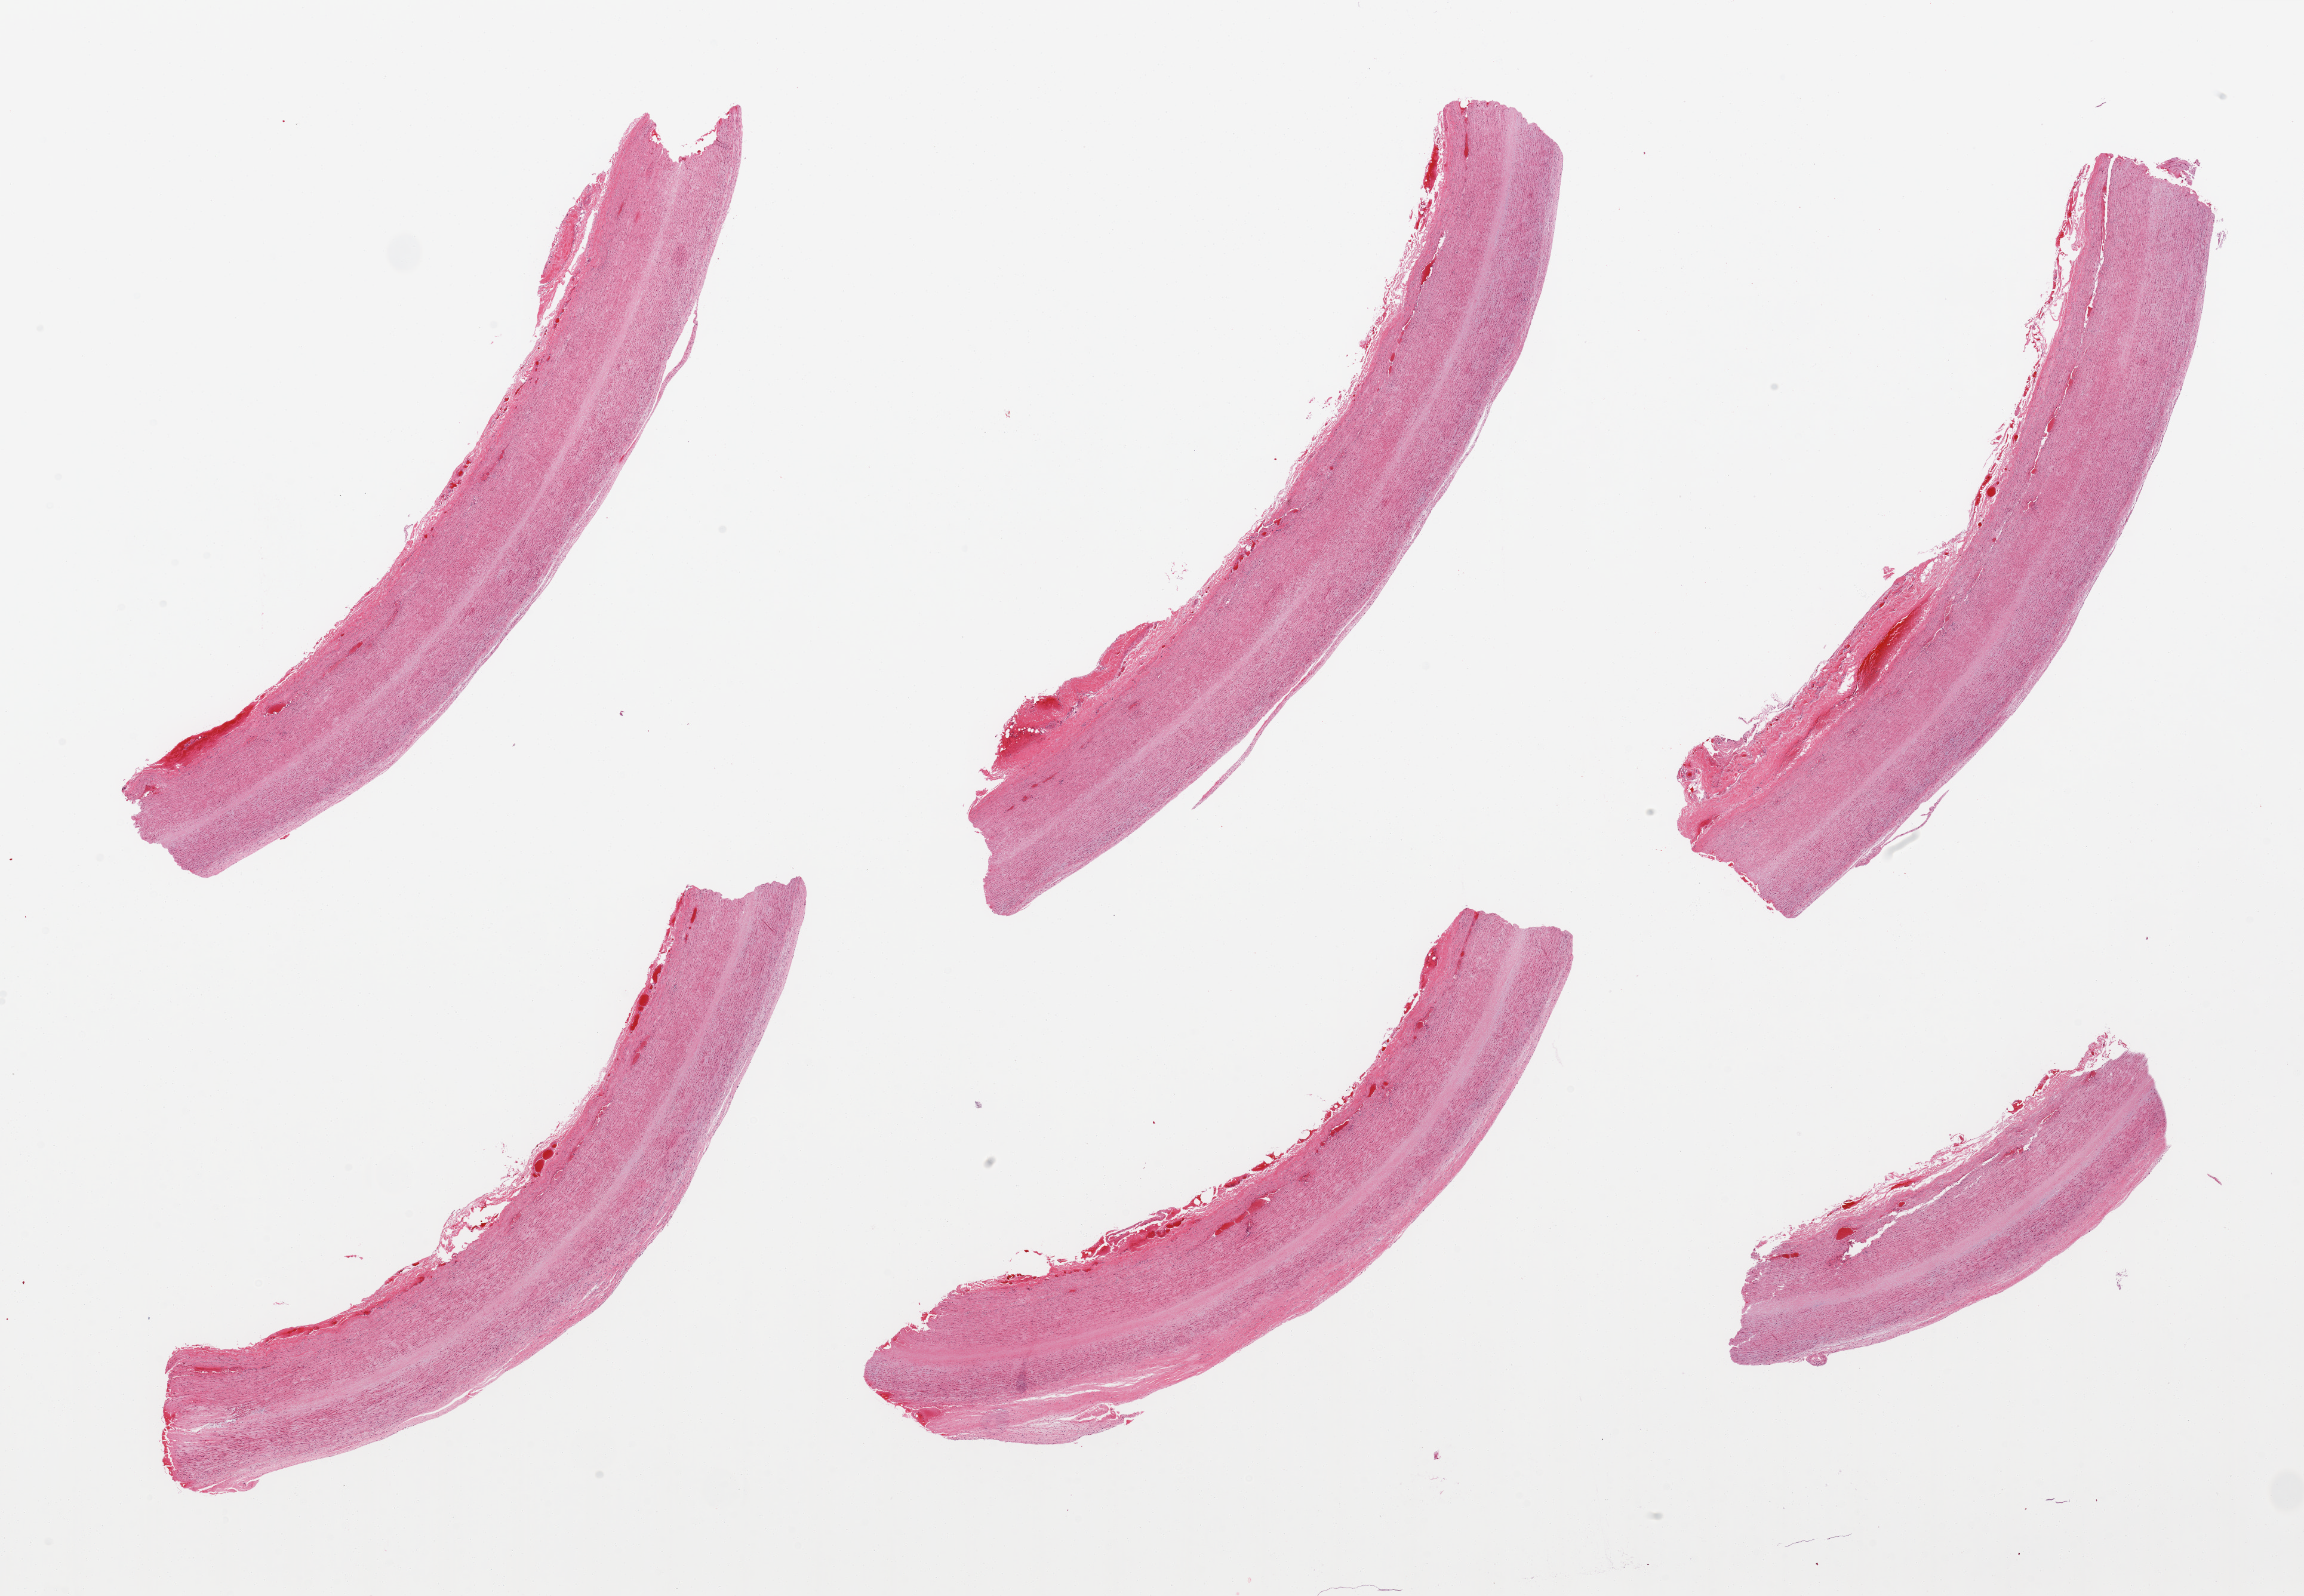
Hematoxylin and eosin (H&E) whole-slide image — a low-resolution overview of the entire scanned area, about 30.5 x 21.1 mm, PAXgene-fixed paraffin-embedded (PFPE) section, target tissue: aorta, donor tissue sample.
Pathologist's review note for this sample: 6 pieces, mural atherosclerotic changes.